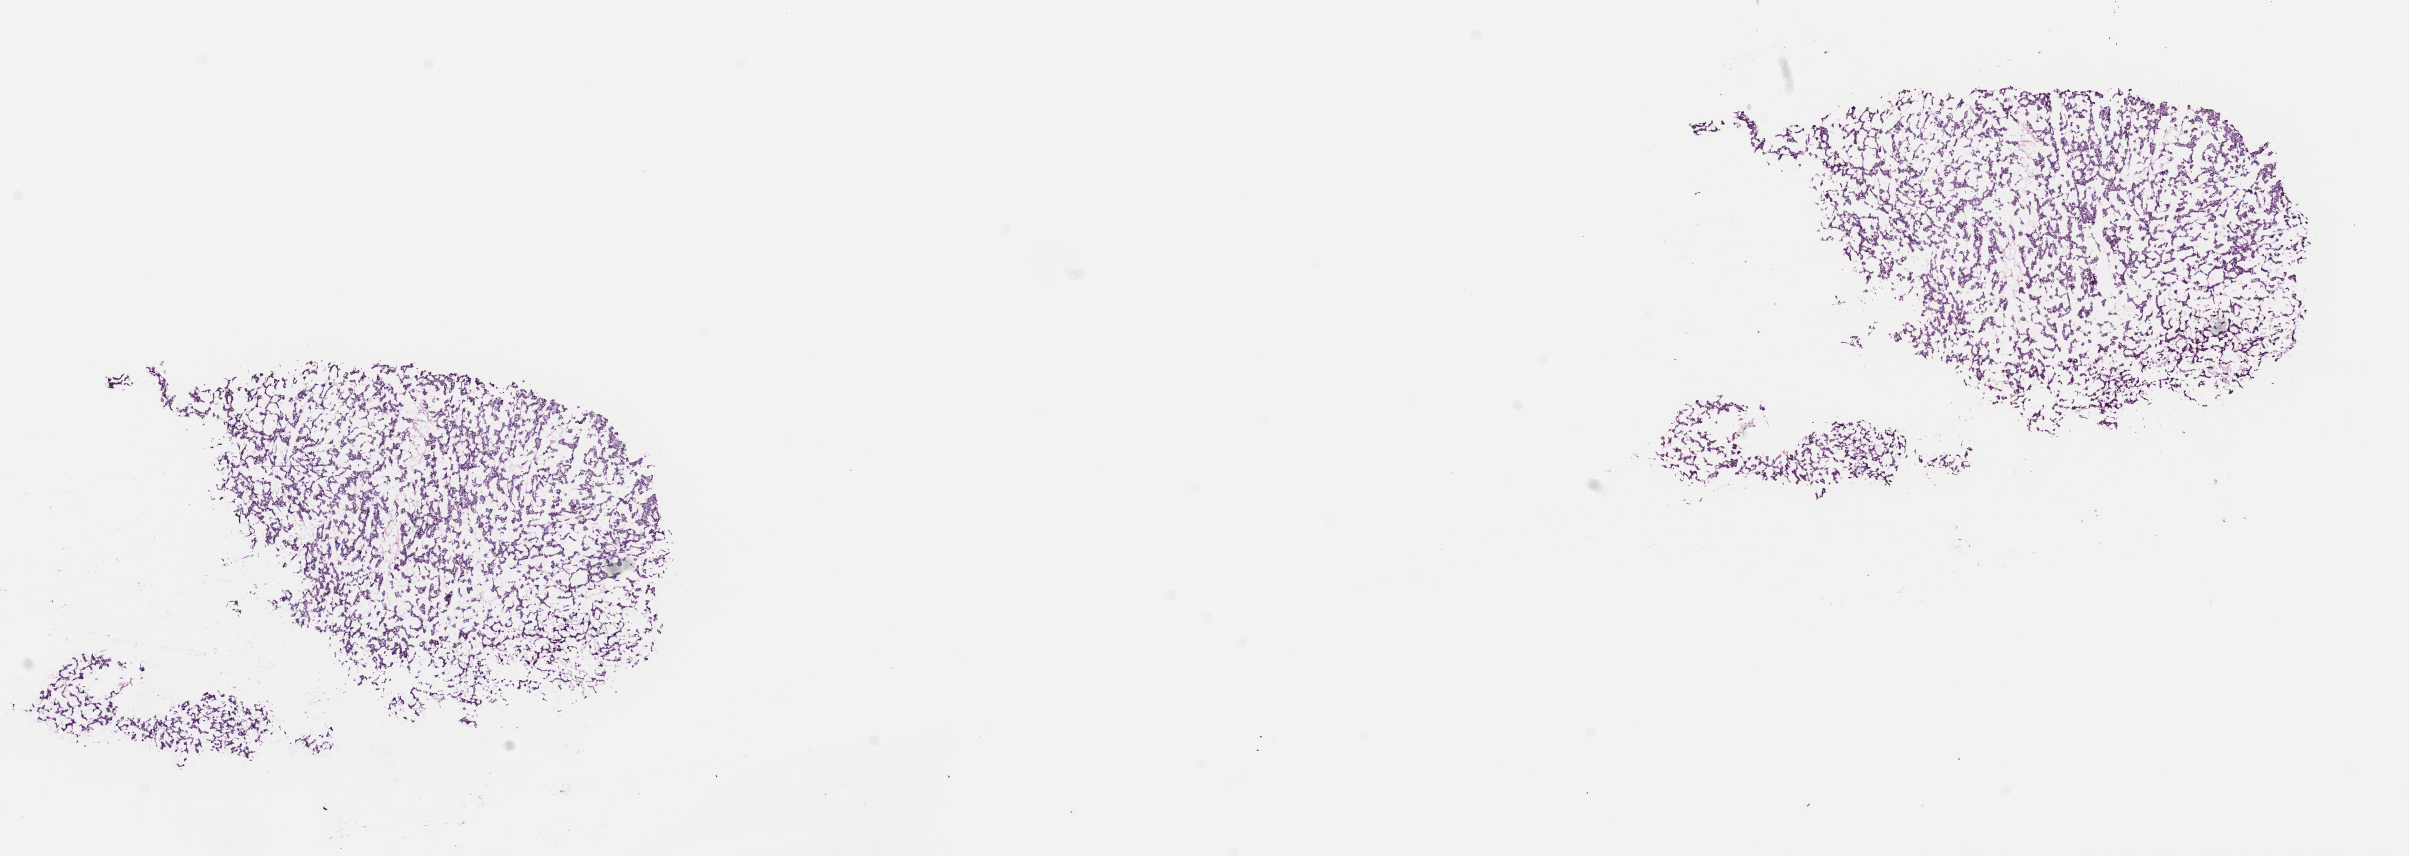
Digitized H&E-stained tissue section (whole slide), shown as a low-resolution overview of the whole scanned area (about 19.0 x 6.8 mm), frozen section from the top of the tissue portion, sample: primary tumour, liver. Female, age 65 years at initial diagnosis. Histologic grade: G1 (well differentiated). Pathologist review of this section (percent, as recorded): tumour cells 97%, tumour nuclei 96%, normal cells 0%, stromal cells 1%, necrosis 2%. Inflammatory infiltration, as recorded: lymphocyte infiltration 1%, monocyte infiltration 0%, neutrophil infiltration 0%.
- pathologic diagnosis: Hepatocellular carcinoma, NOS
- AJCC pathologic stage: IIIA (7th edition)